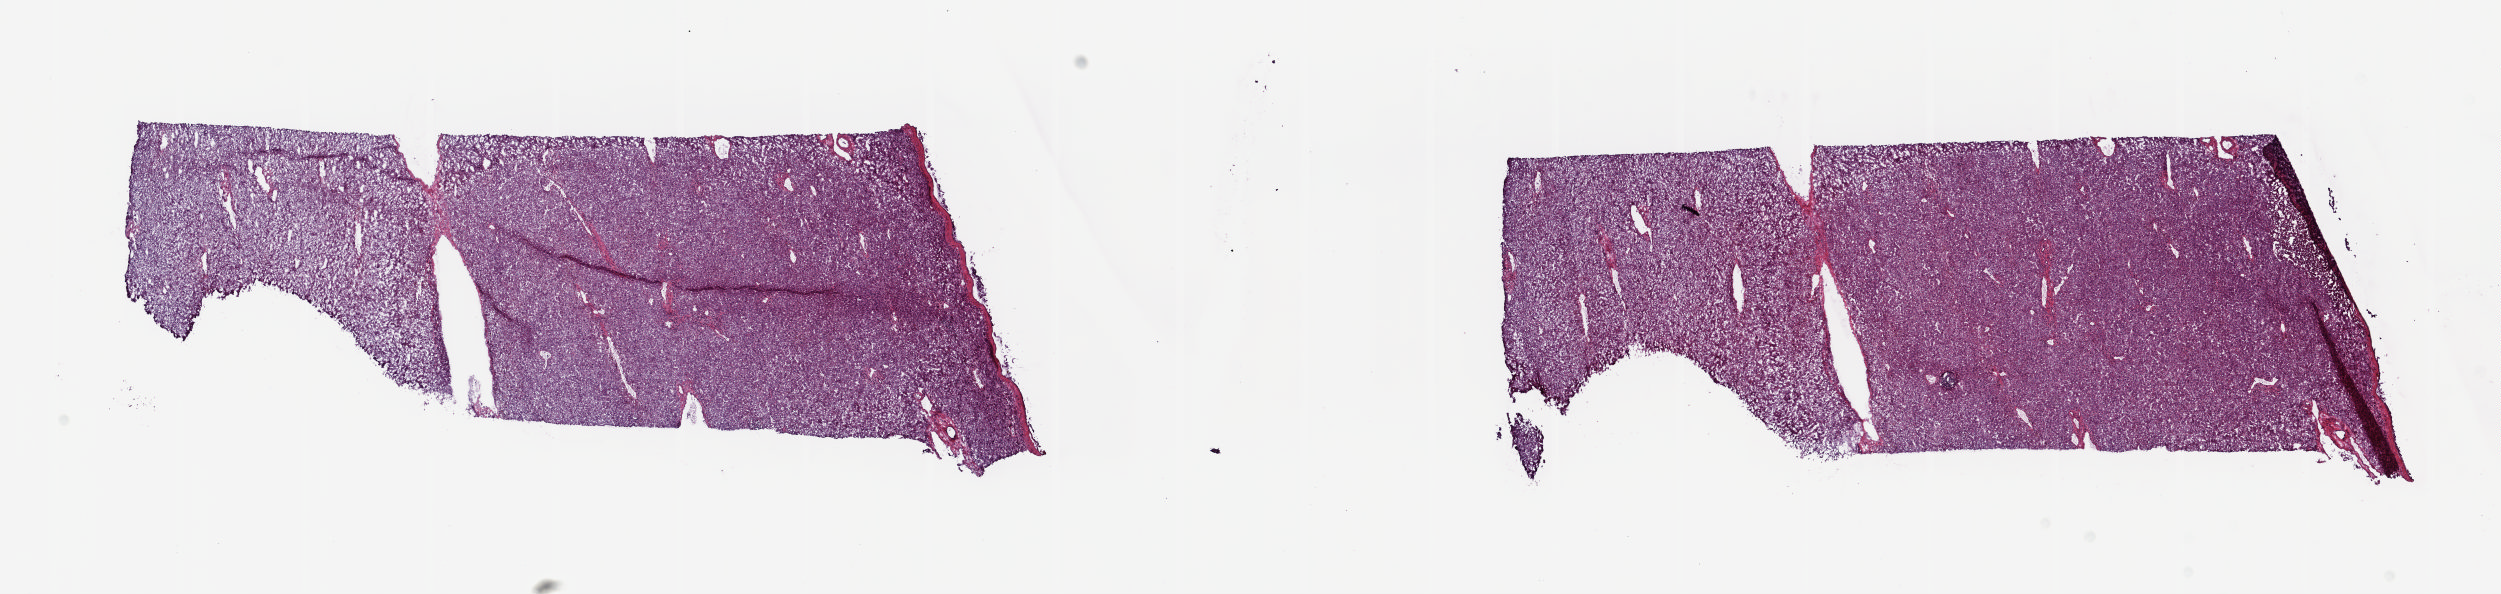
H&E whole-slide image — a low-resolution overview of the entire scanned area, about 19.8 x 4.7 mm, frozen section from the top of the tissue portion, solid tissue normal (non-tumour tissue) sample from the liver. Female, age 71 years at initial diagnosis. Pathologist review of this section (percent, as recorded): tumour cells 0%, tumour nuclei 0%, normal cells 85%, stromal cells 15%, necrosis 0%. Infiltration values recorded for this section: lymphocyte infiltration 5%, monocyte infiltration 0%, neutrophil infiltration 0%.
This section: solid tissue normal (non-tumour) sample from the same patient. Patient diagnosis: Hepatocellular carcinoma, NOS.